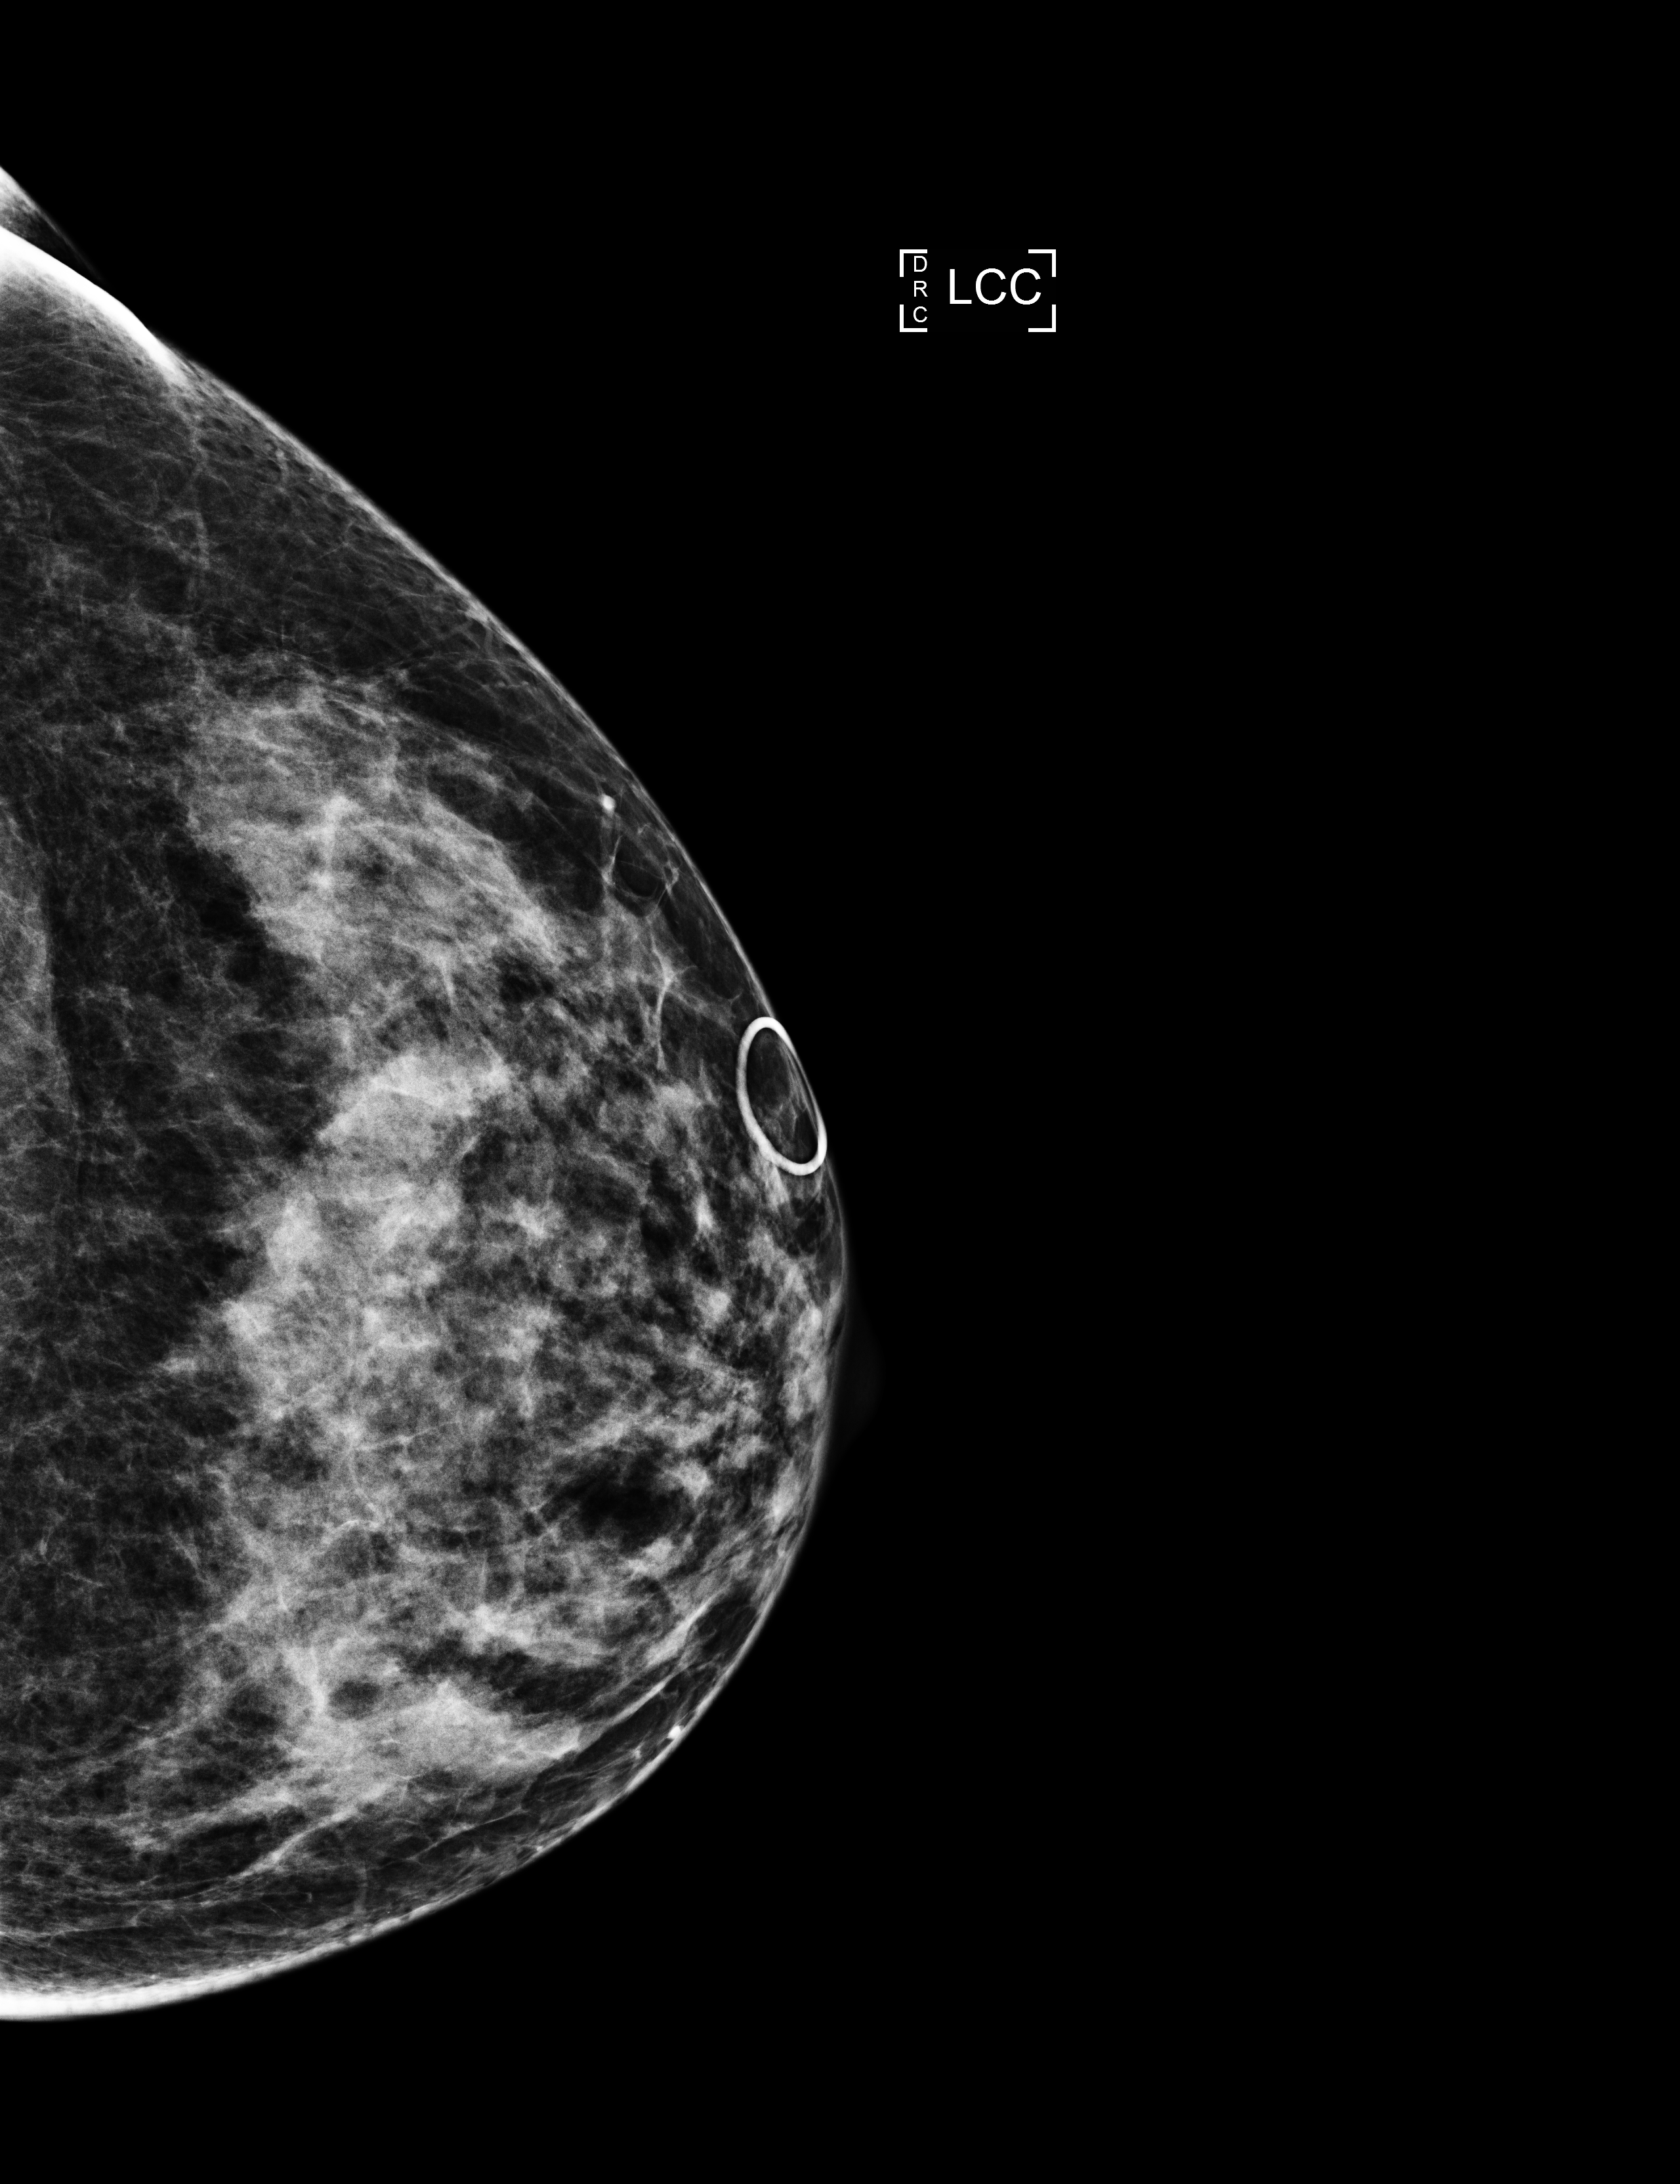
Digital mammogram (FFDM), left breast, cranio-caudal projection, annual screening mammography examination. Female patient, age 60 years.
Final BI-RADS assessment for this screening round (tomosynthesis exam, both breasts): category 1.